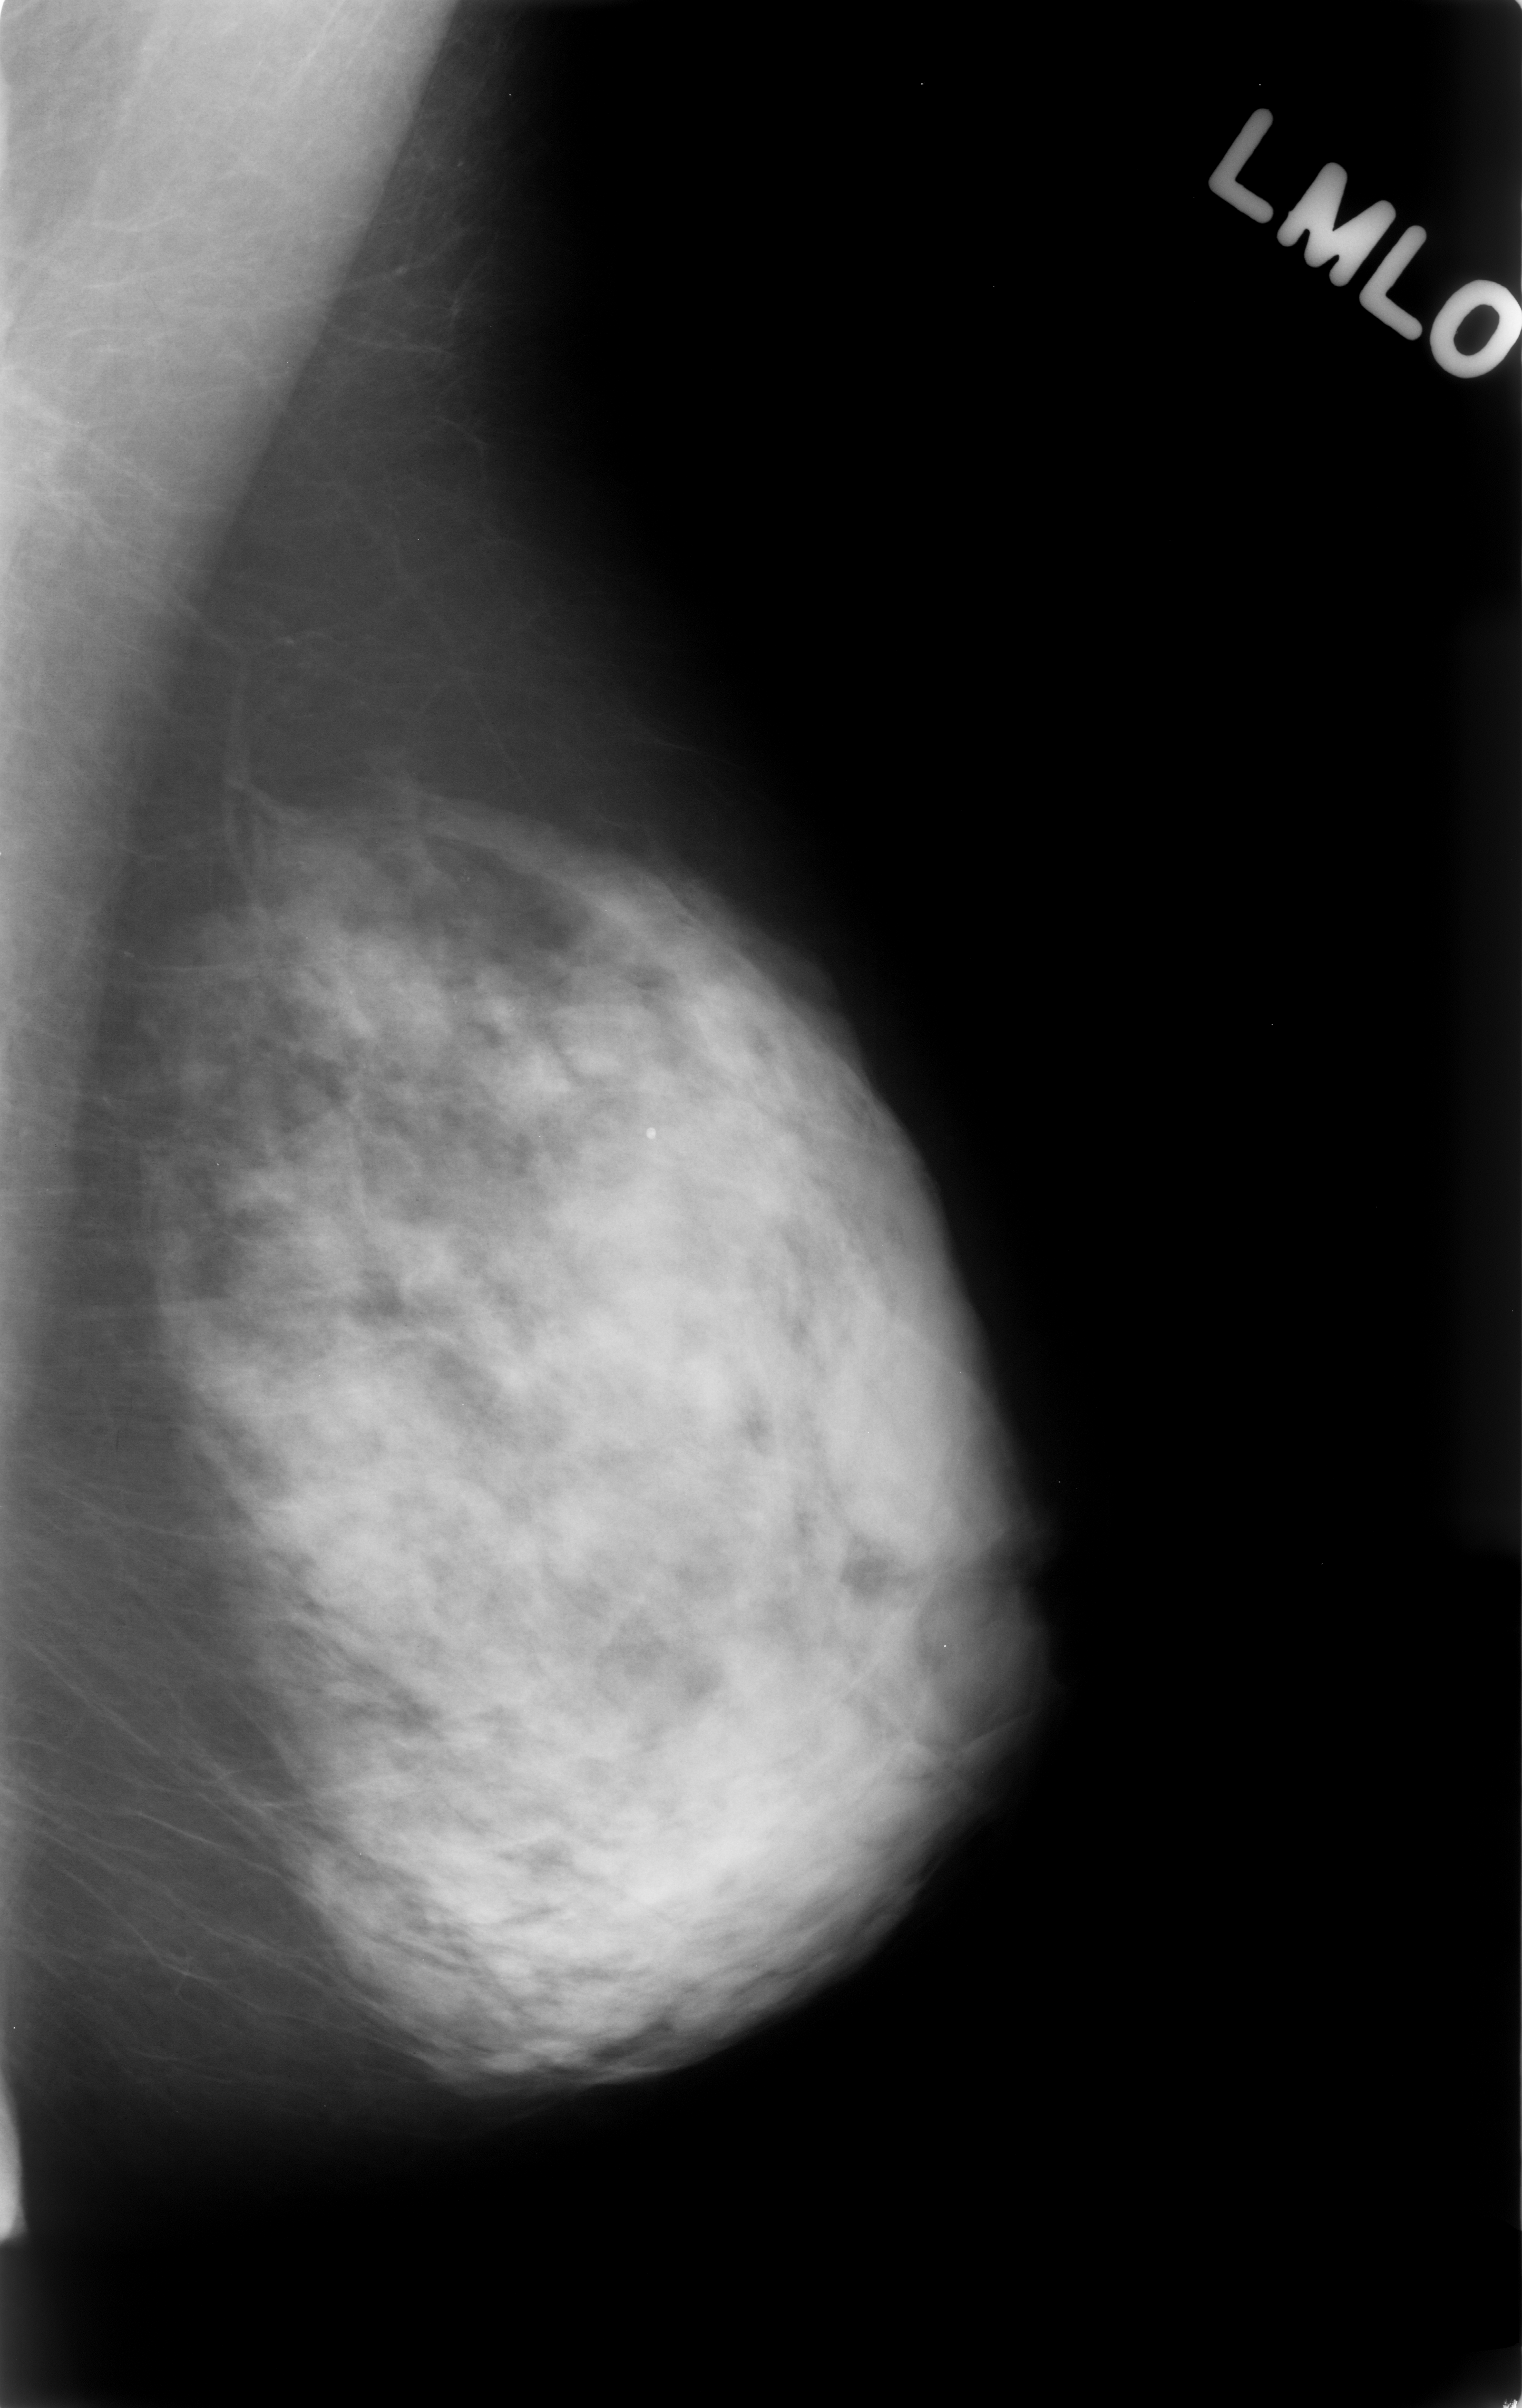
Scanned film-screen mammogram, left breast, MLO view, BI-RADS breast density category 4 (scale 1–4).
Marked abnormality: calcifications, morphology amorphous, distribution segmental; BI-RADS assessment category 4; subtlety rating 2 on a 1 (subtle) to 5 (obvious) scale; pathology (as recorded): benign.